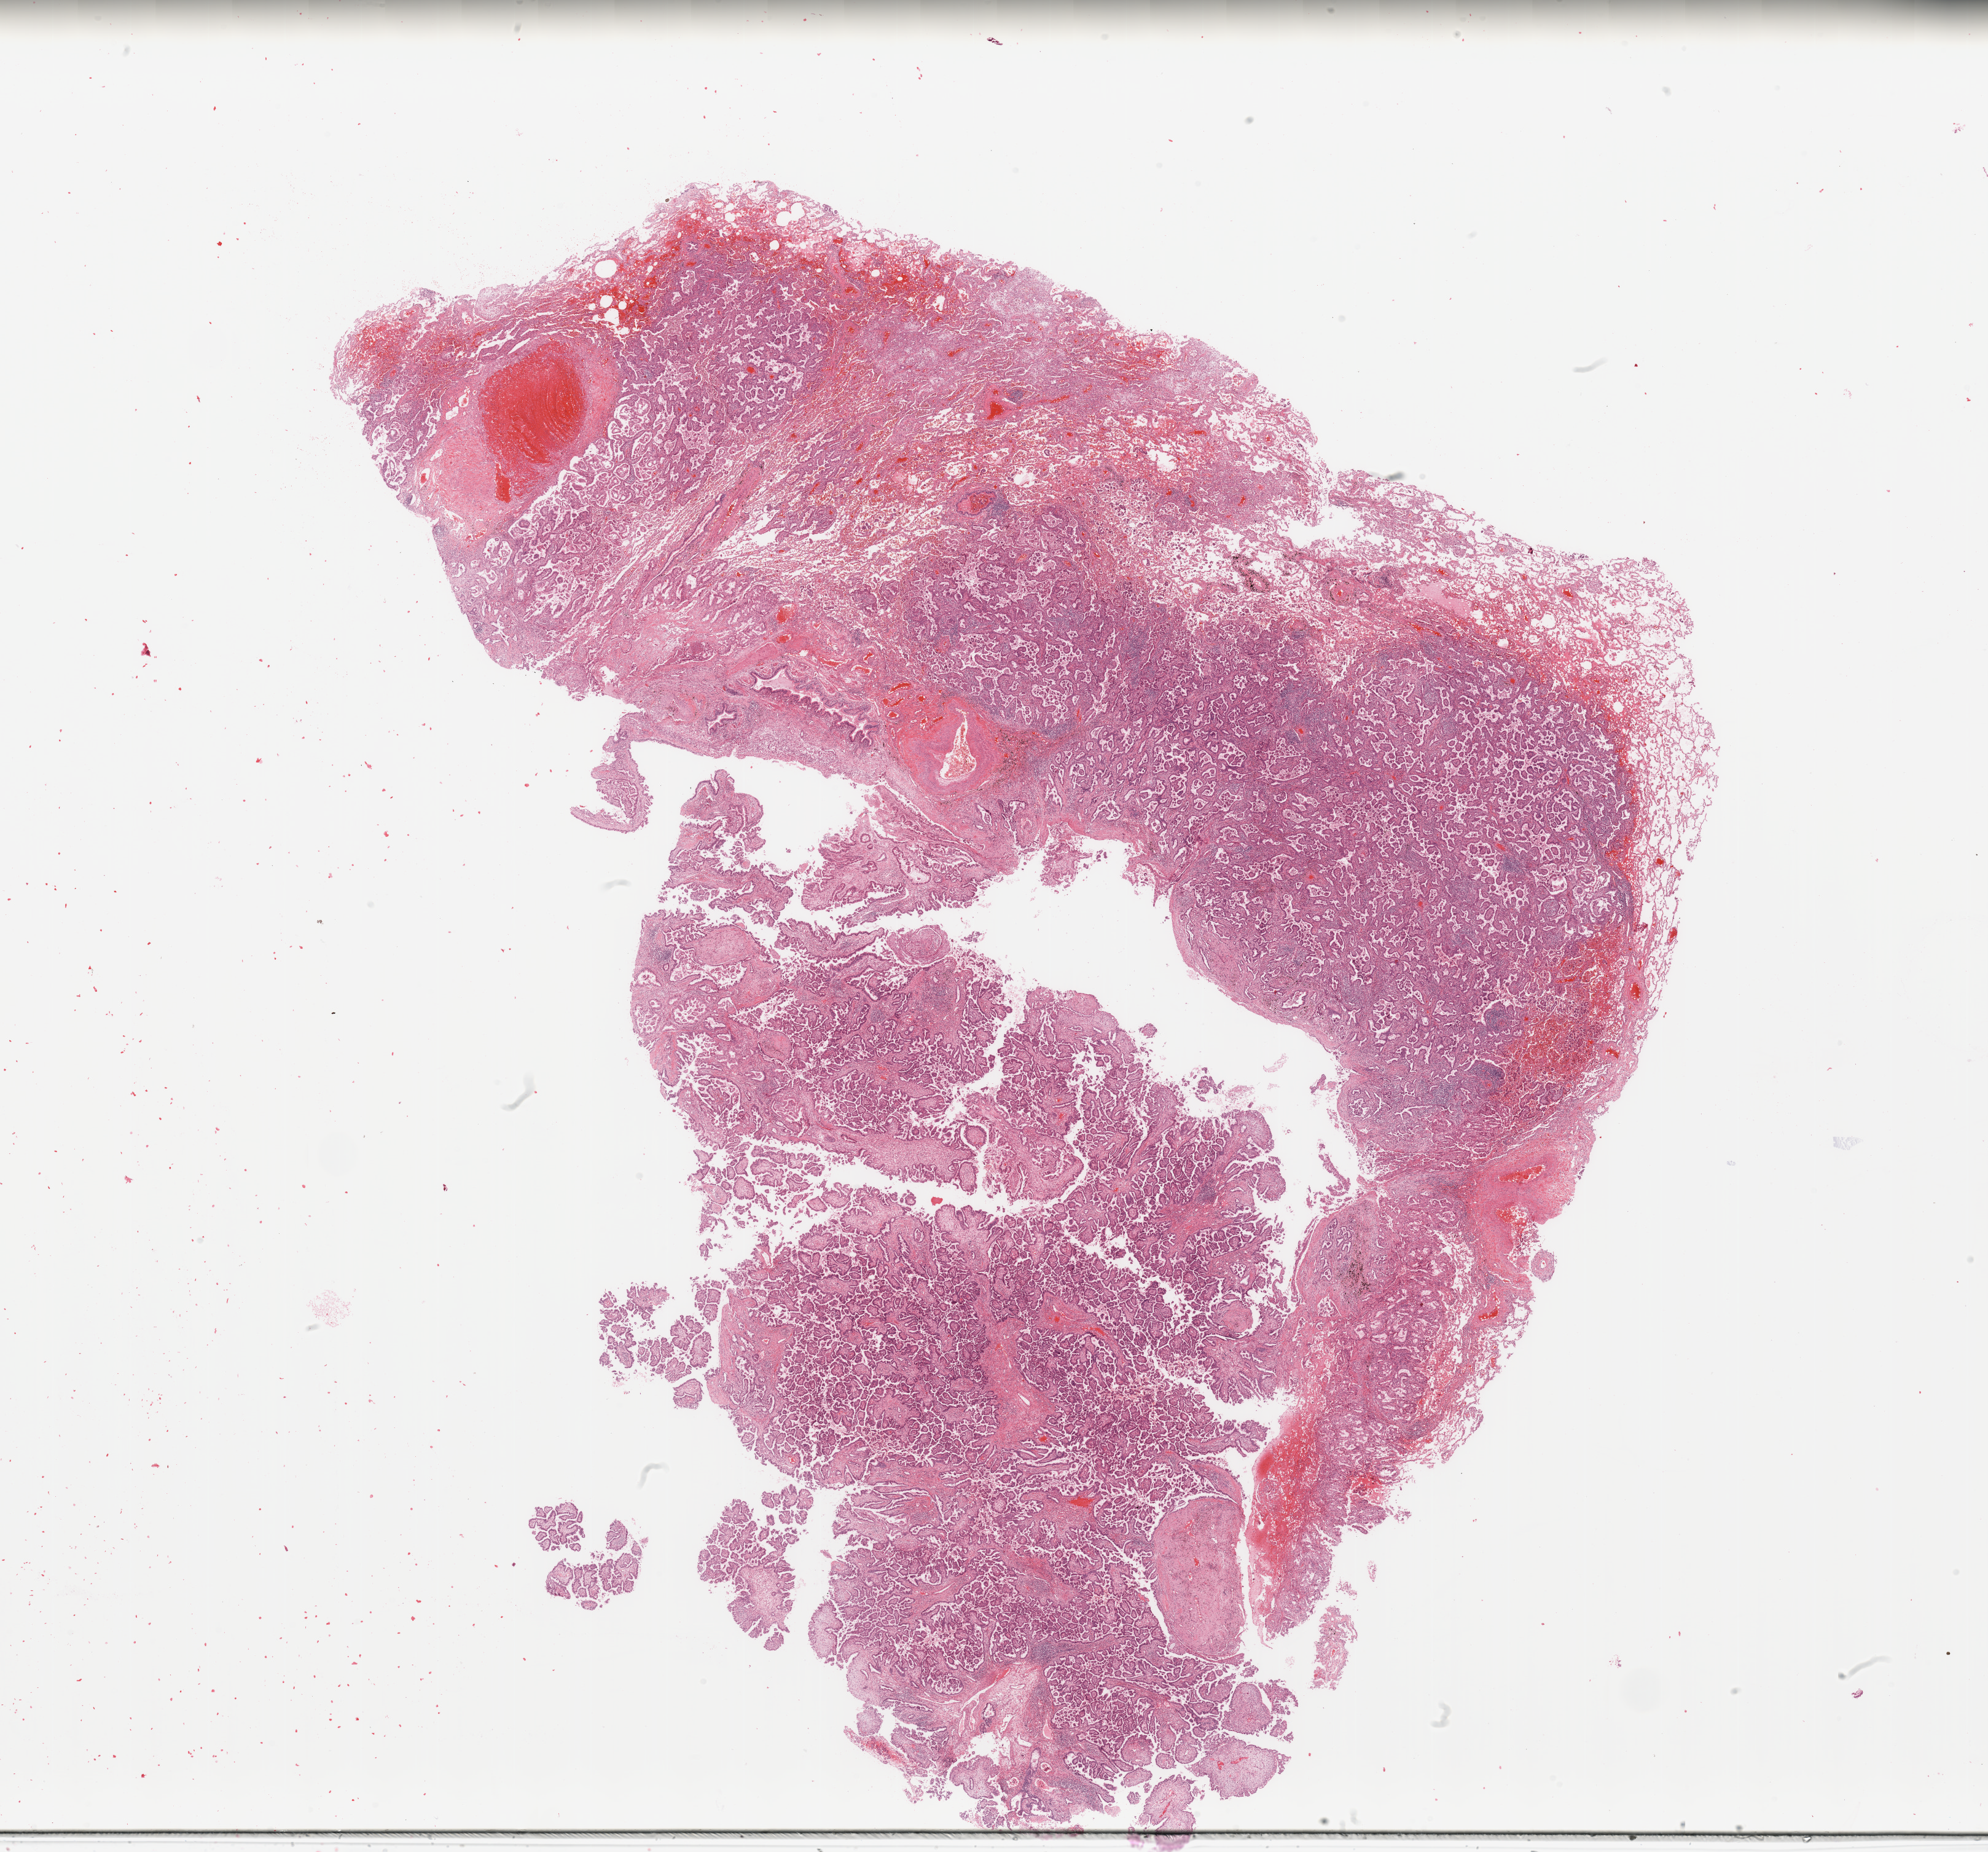
Digitized H&E tissue section (whole slide), shown as a low-resolution overview of the whole scanned area (about 25.6 x 23.8 mm). Tumour tissue sample, lung. 60-year-old female patient.
Histologic diagnosis: Adenocarcinoma, NOS.